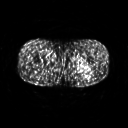
FDG PET of an extremity soft-tissue mass (from a PET/CT study), one axial slice; position 241 of 267 along the scan axis; 3.27 mm slice thickness; 128 × 128 image matrix, field of view 500 × 500 mm. Male patient, age 27 years. Case-level facts recorded for this patient, not image findings: histological type: extraskeletal osteosarcoma; grade: high; site of the primary tumour: left adductur.
Outlined on this slice (expert contour drawn on MRI and transferred to this co-registered scan by the dataset authors):
- gross tumour volume (mass): bounding box (x1, y1, x2, y2) in pixels: (70, 61, 95, 75)